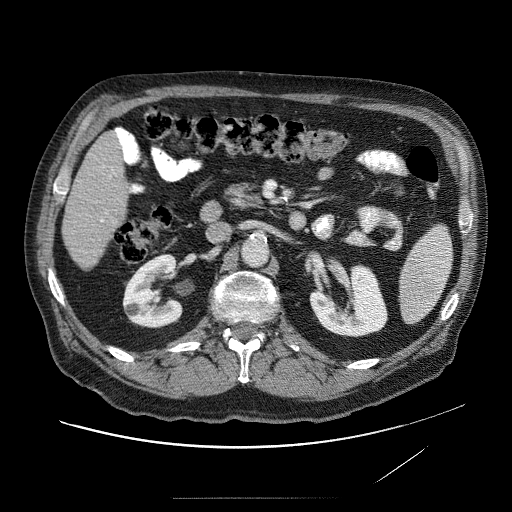
Contrast-enhanced abdominal CT (liver protocol), one axial slice. Reconstruction kernel STANDARD. 120 kVp. Soft-tissue window (W 400 / L 40 HU). 2.5 mm slice thickness. 512 × 512 image matrix, field of view 420 × 420 mm. Case-level facts recorded for this patient, not image findings: diagnosis: hepatocellular carcinoma (patient treated with transarterial chemoembolisation; whether this scan precedes or follows treatment is not stated here); TNM stage (as recorded): Stage-IVA; Child-Pugh class: A.
Annotated regions visible in this slice (semi-automatically segmented with operator editing):
- liver parenchyma outside the tumour (the mass and vessels are separate outlines, so this box may not span the whole liver): bounding box <62,124,134,271> (left, top, right, bottom; pixels)
- liver vessels: <94,127,128,244>